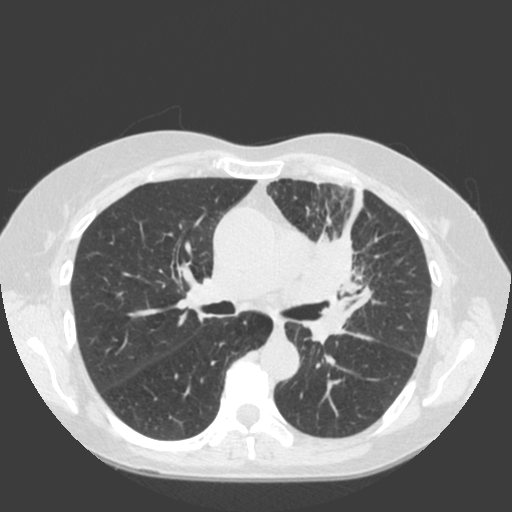
Low-dose screening chest CT, axial slice. First (baseline) screen. Lung window (W 1500 / L -600 HU). Standard (soft-tissue) reconstruction kernel (C). Slice 70 of 184 in the series. Female, age 66 years at enrolment. Current smoker at enrolment.
Expert reader's lesion annotation, box from (x=278, y=207) to (x=402, y=319) px. The exam's reader record, not a measurement of the box and not confirmed to be the same lesion: non-calcified nodule or mass ≥4 mm, left upper lobe, 61 × 45 mm, spiculated (stellate) margins, soft tissue attenuation. Participant outcome: lung cancer diagnosed 19 days after this screen — squamous cell carcinoma, keratinizing, NOS, left upper lobe, left hilum, mediastinum, left main stem bronchus, other location, poorly differentiated (G3), stage IIIB (AJCC 6th edition), 60 mm at pathology.